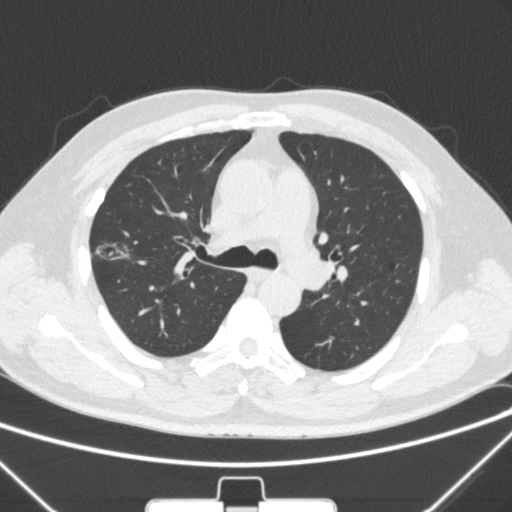
Chest CT, one axial slice; position 200 of 320 along the scan axis; 120 kVp; lung window (W 1500 / L -600 HU); 1 mm slice thickness; 512 × 512 image matrix, field of view 350 × 350 mm. Male patient, age 58 years. Case-level facts recorded for this patient, not image findings: clinical TNM (as recorded): T1c N0 M0; histopathological grade: G2.
Annotated regions visible in this slice (rectangle marked by the reading radiologist):
- lung tumour (recorded histology: adenocarcinoma): bounding box <87,229,134,273> (left, top, right, bottom; pixels)